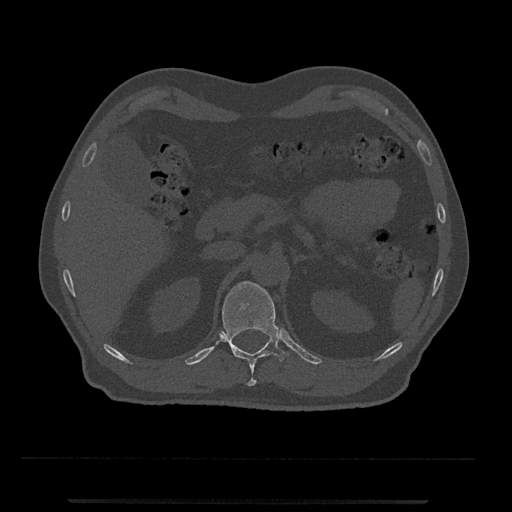
CT including the spine, one axial slice; position 398 of 797 along the scan axis; reconstruction kernel Br40s/3; 120 kVp; bone window (W 1800 / L 400 HU); 512 × 512 image matrix, field of view 419 × 419 mm. Patient: male, 63 years. Case-level facts recorded for this patient, not image findings: primary cancer: prostate.
Annotated regions visible in this slice (semi-automatically segmented with operator editing):
- T12 vertebra: bounding box <222,281,288,386> (left, top, right, bottom; pixels)